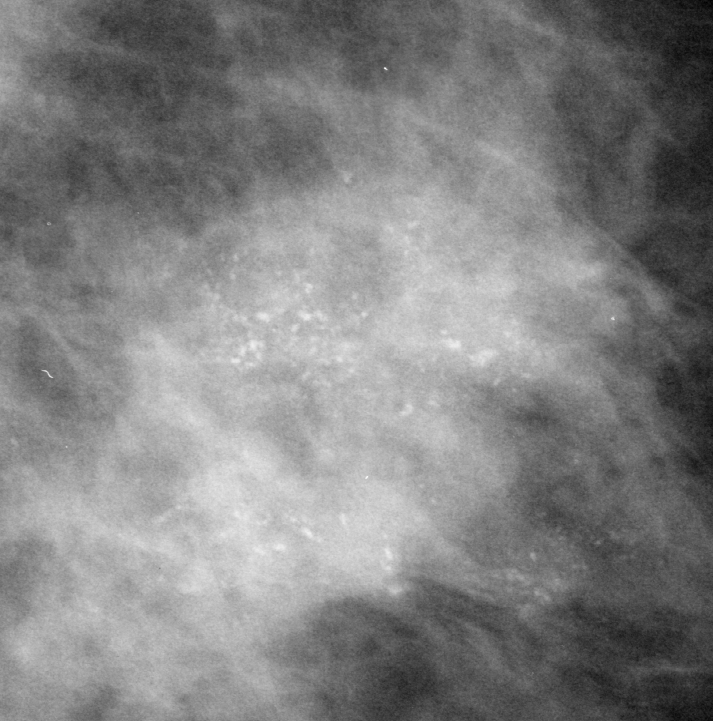
Region of interest cut from a scanned film mammogram (one marked finding), left breast, MLO view, BI-RADS breast density category 2 (scale 1–4).
Finding: calcifications, morphology pleomorphic, distribution segmental; BI-RADS assessment category 5; subtlety rating 5 on a 1 (subtle) to 5 (obvious) scale; pathology result (as recorded, not read from the image): malignant.